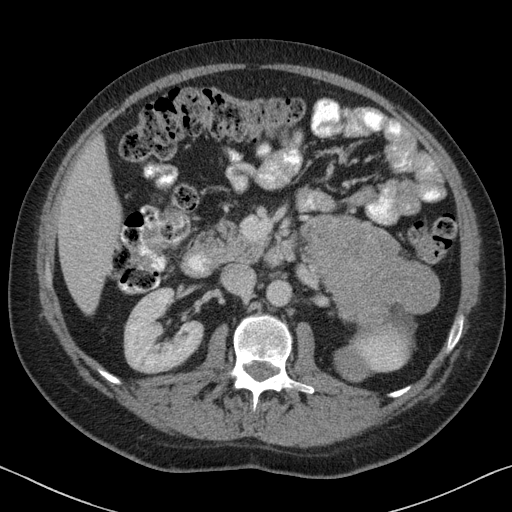
Contrast-enhanced abdominal CT, one axial slice. Slice 36 of 88 in the series (ordered by position). Reconstruction kernel B31f. Soft-tissue window (W 400 / L 40 HU). 512 × 512 image matrix. Male patient, age 51 years. From the clinical record (not read from this slice): diagnosis: adrenocortical carcinoma; tumour side: left adrenal; tumour size at pathology: 16.5 cm; Ki-67 index: 30 %; stage (as recorded): 2.
Outlined on this slice (semi-automatically segmented with operator editing):
- mass: bounding box (x1, y1, x2, y2) in pixels: (304, 217, 438, 377)